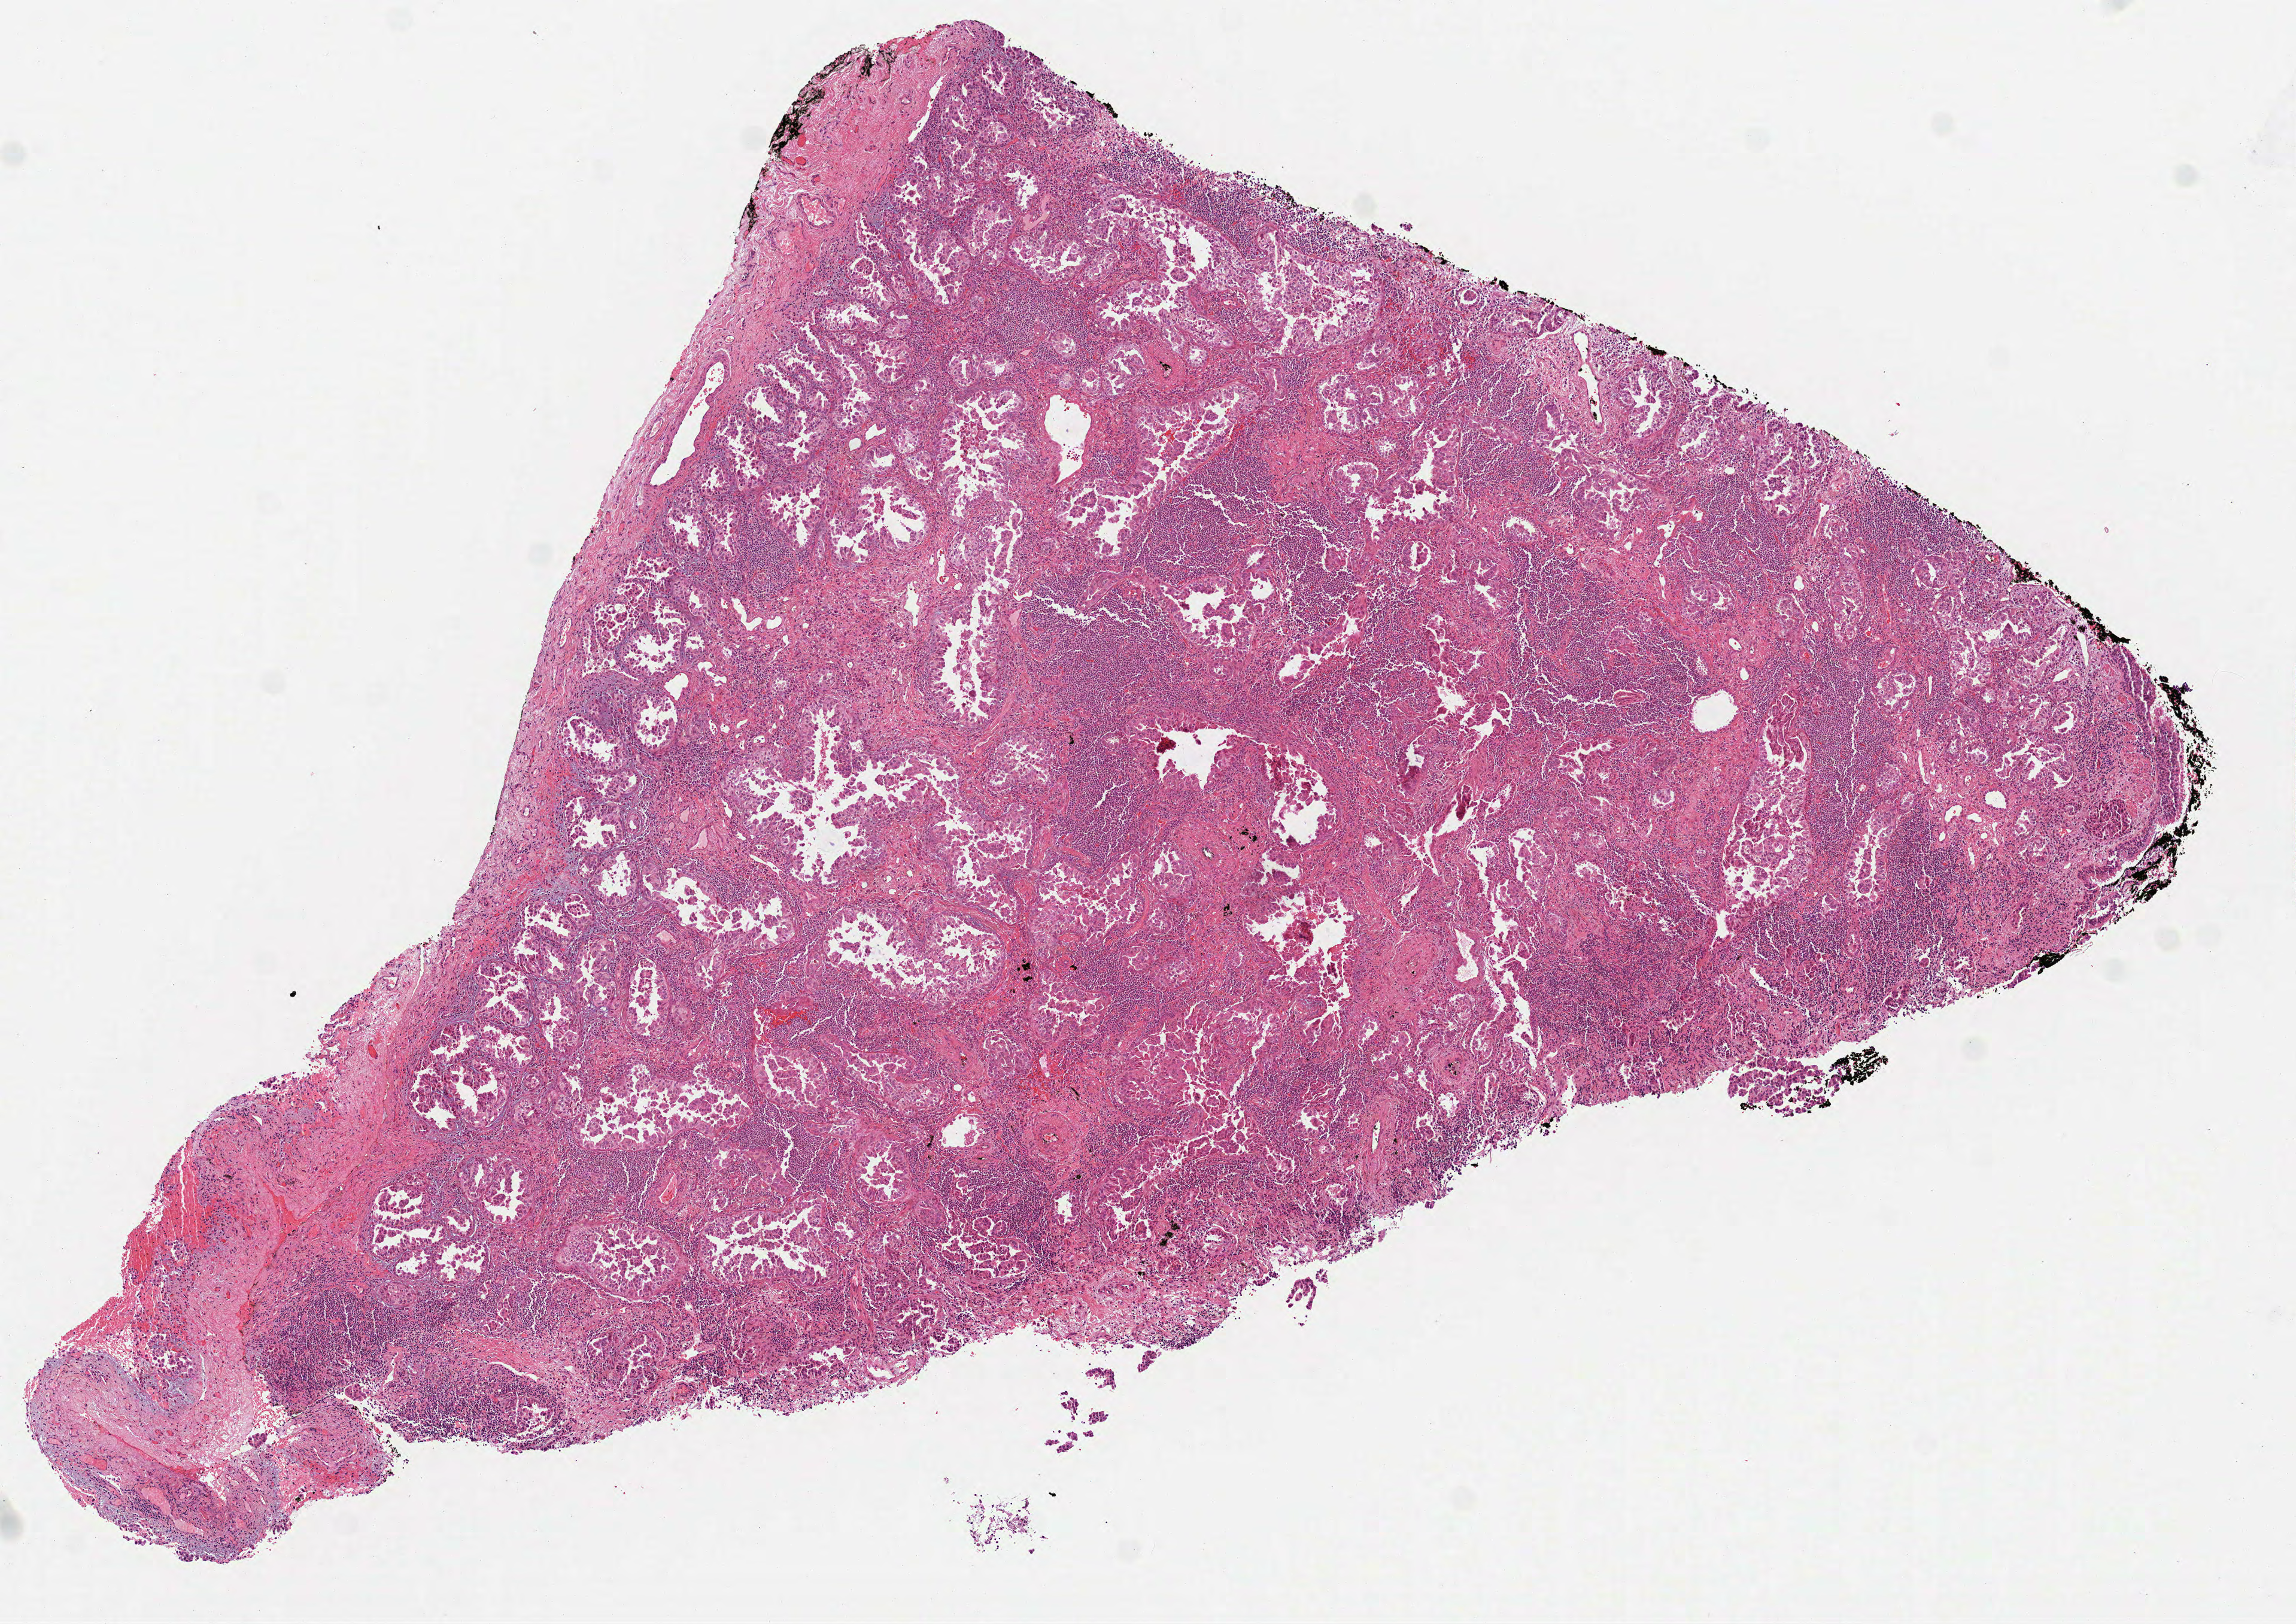
Whole-slide histology image, H&E-stained — whole scanned area (about 7.7 x 5.5 mm) shown as a low-resolution overview. Formalin-fixed paraffin-embedded (FFPE) diagnostic section. Sample: primary tumour, lung. Female, age 63 years at initial diagnosis.
- histologic diagnosis: Adenocarcinoma, NOS (lower lobe, lung)
- laterality: left
- AJCC pathologic stage: IIA (7th edition)